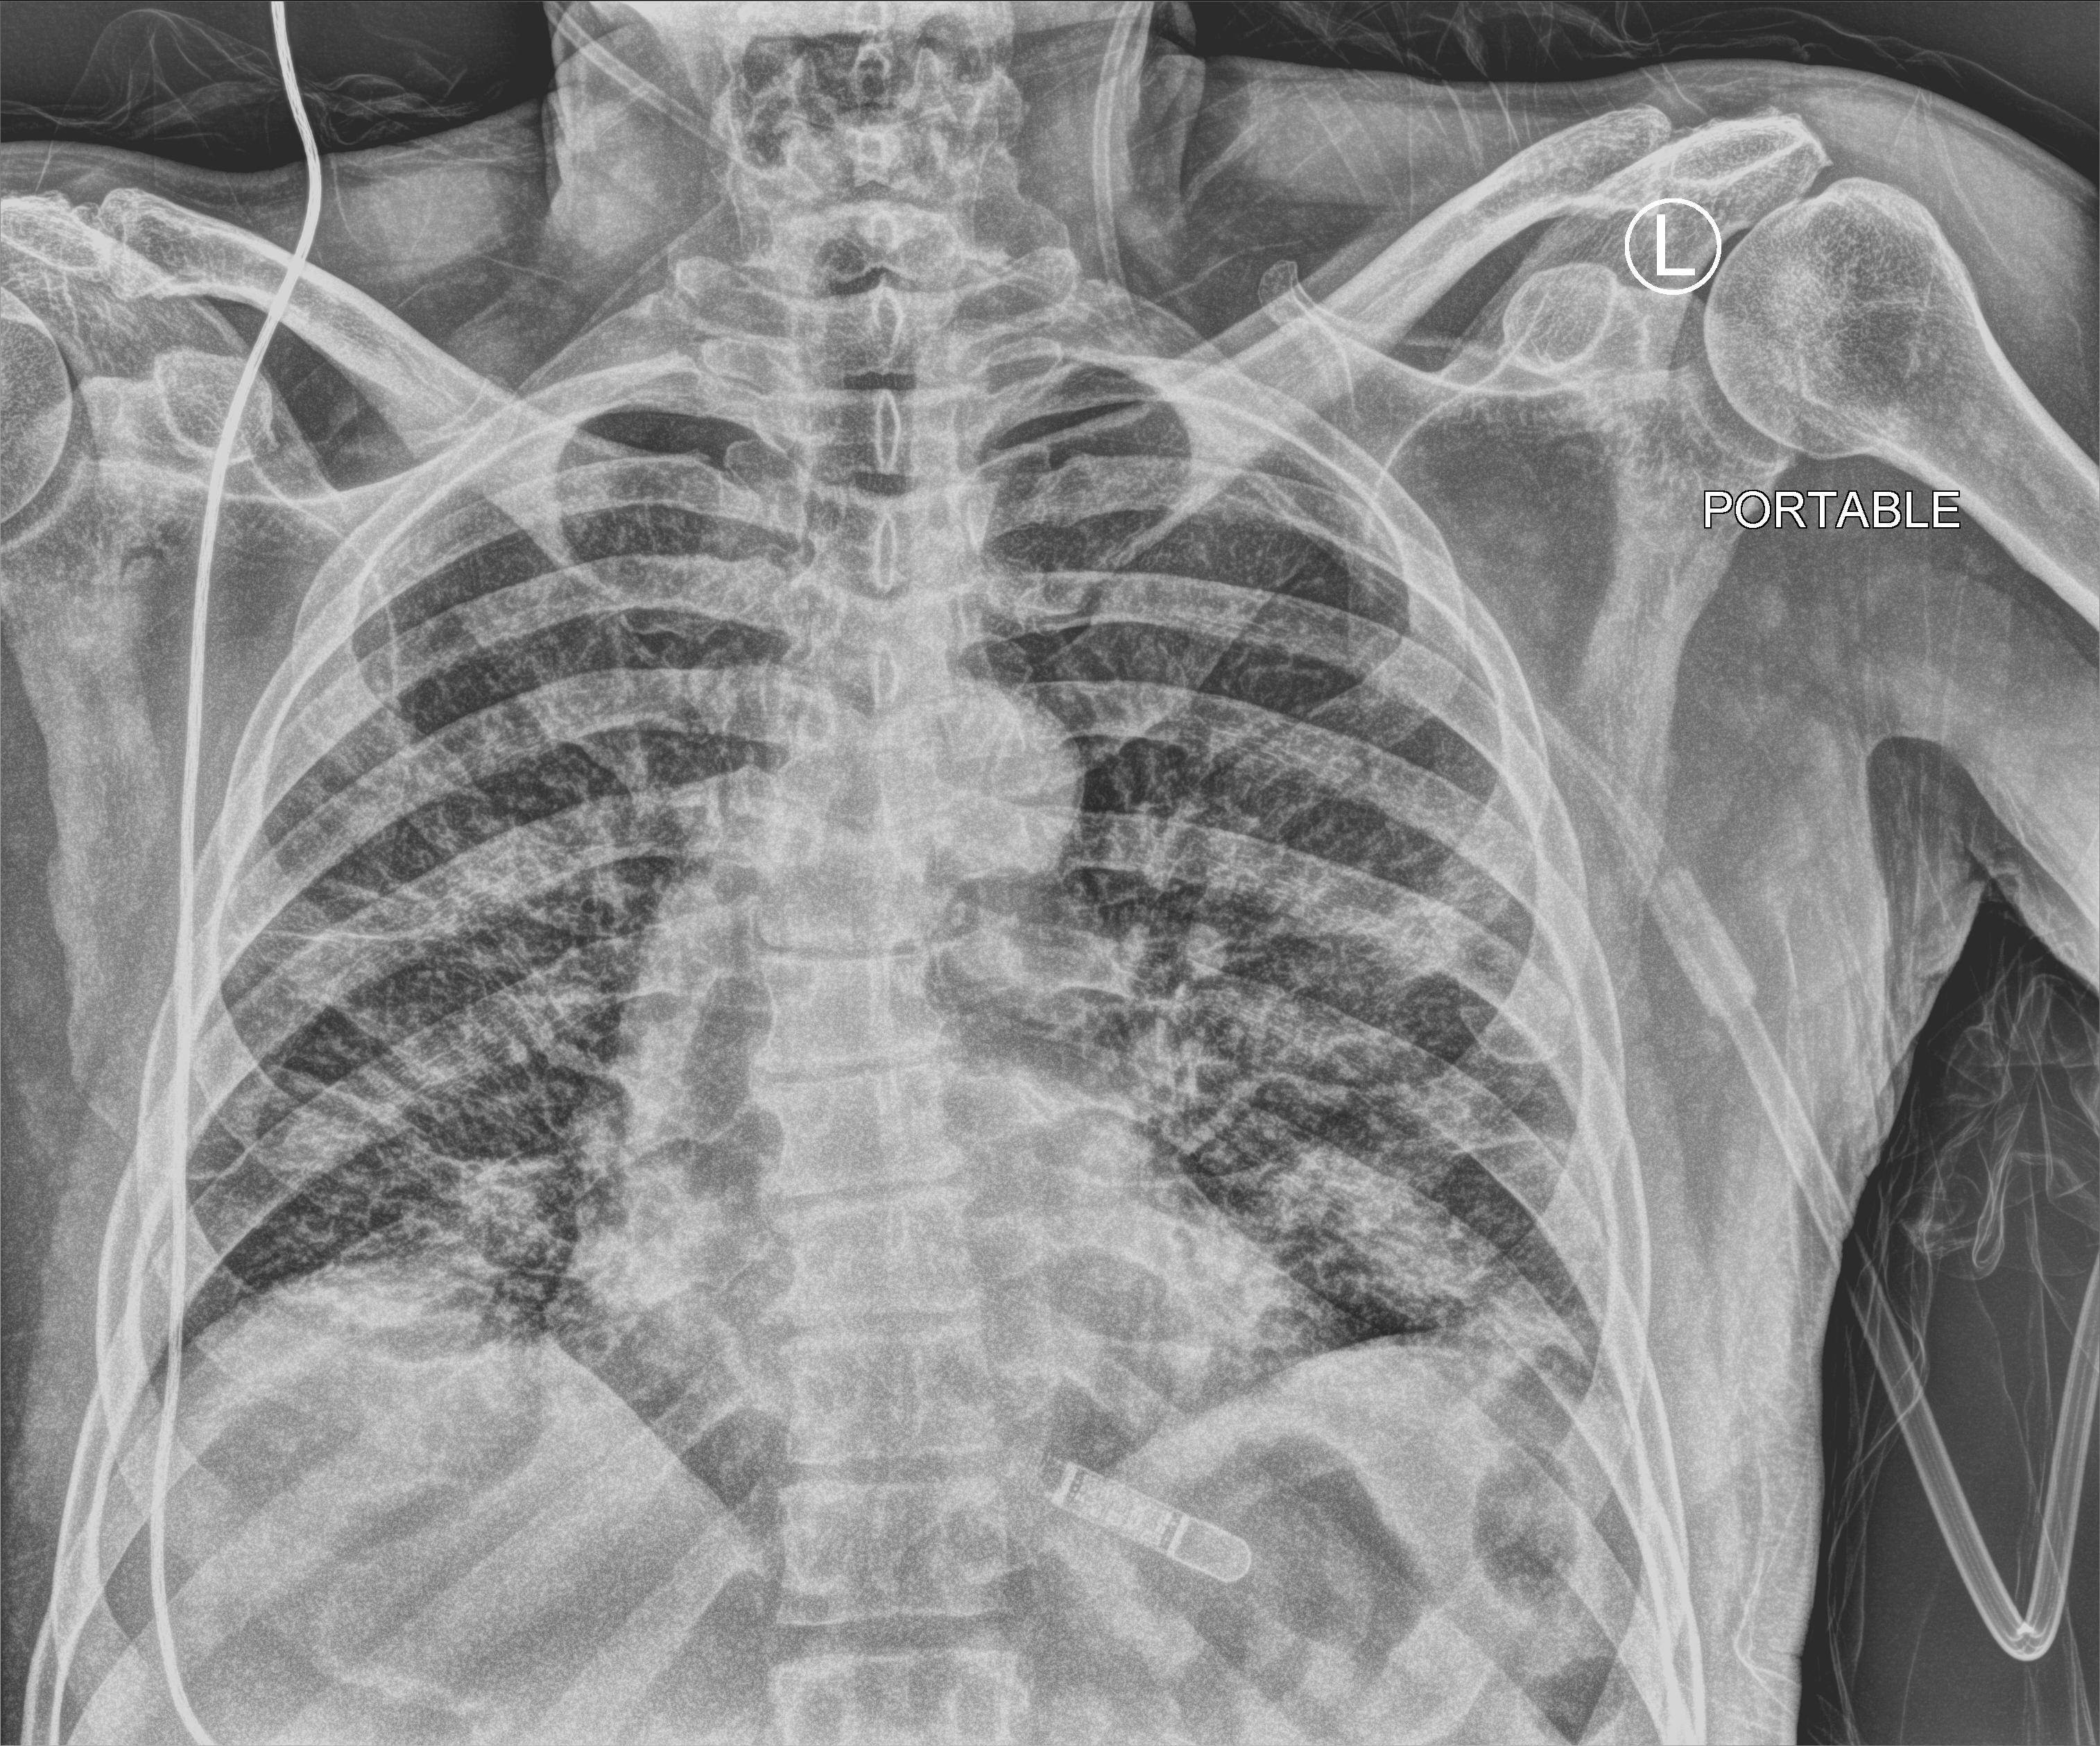
Chest X-ray (portable). Male patient hospitalised with COVID-19, age 75–90 years.
Hospital-stay facts (about this admission, not read from this image; timing relative to this image not recorded): mechanically ventilated during this hospital stay: no.